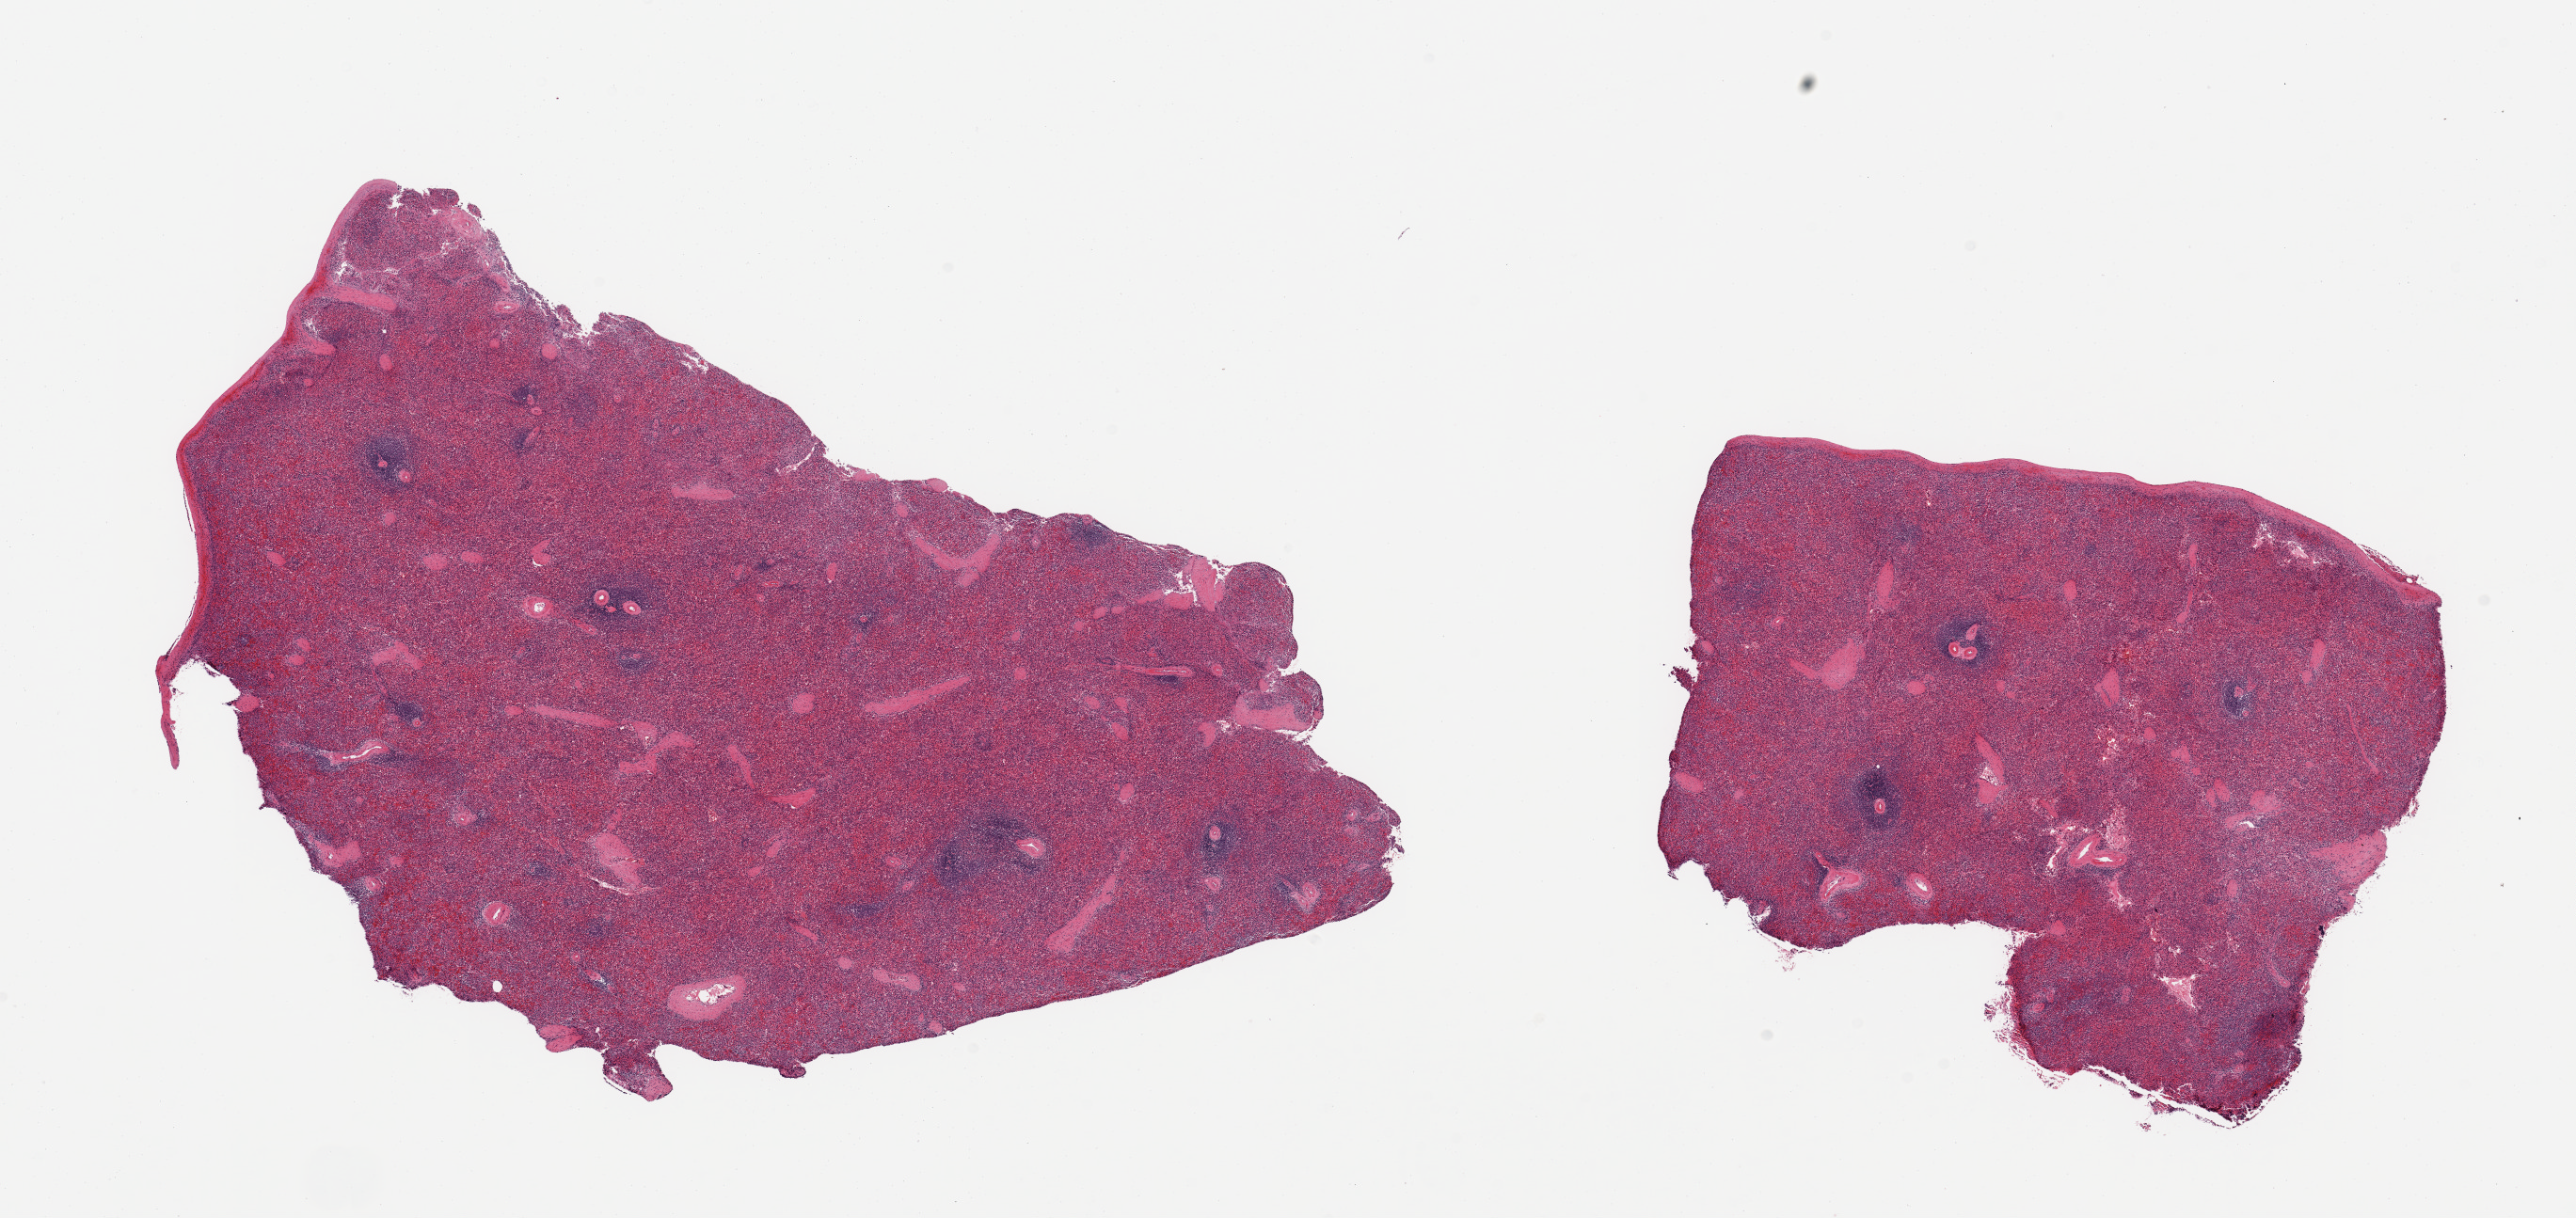
Digitized haematoxylin and eosin-stained section — low-resolution overview of the scanned area, about 21.7 x 10.2 mm (acquisition: 20x scan). PAXgene-fixed, paraffin-embedded tissue. Section of spleen (target tissue). Tissue donor sample. Donor sex: male.
Reviewer comment on this tissue sample: 2 pieces; congestion.